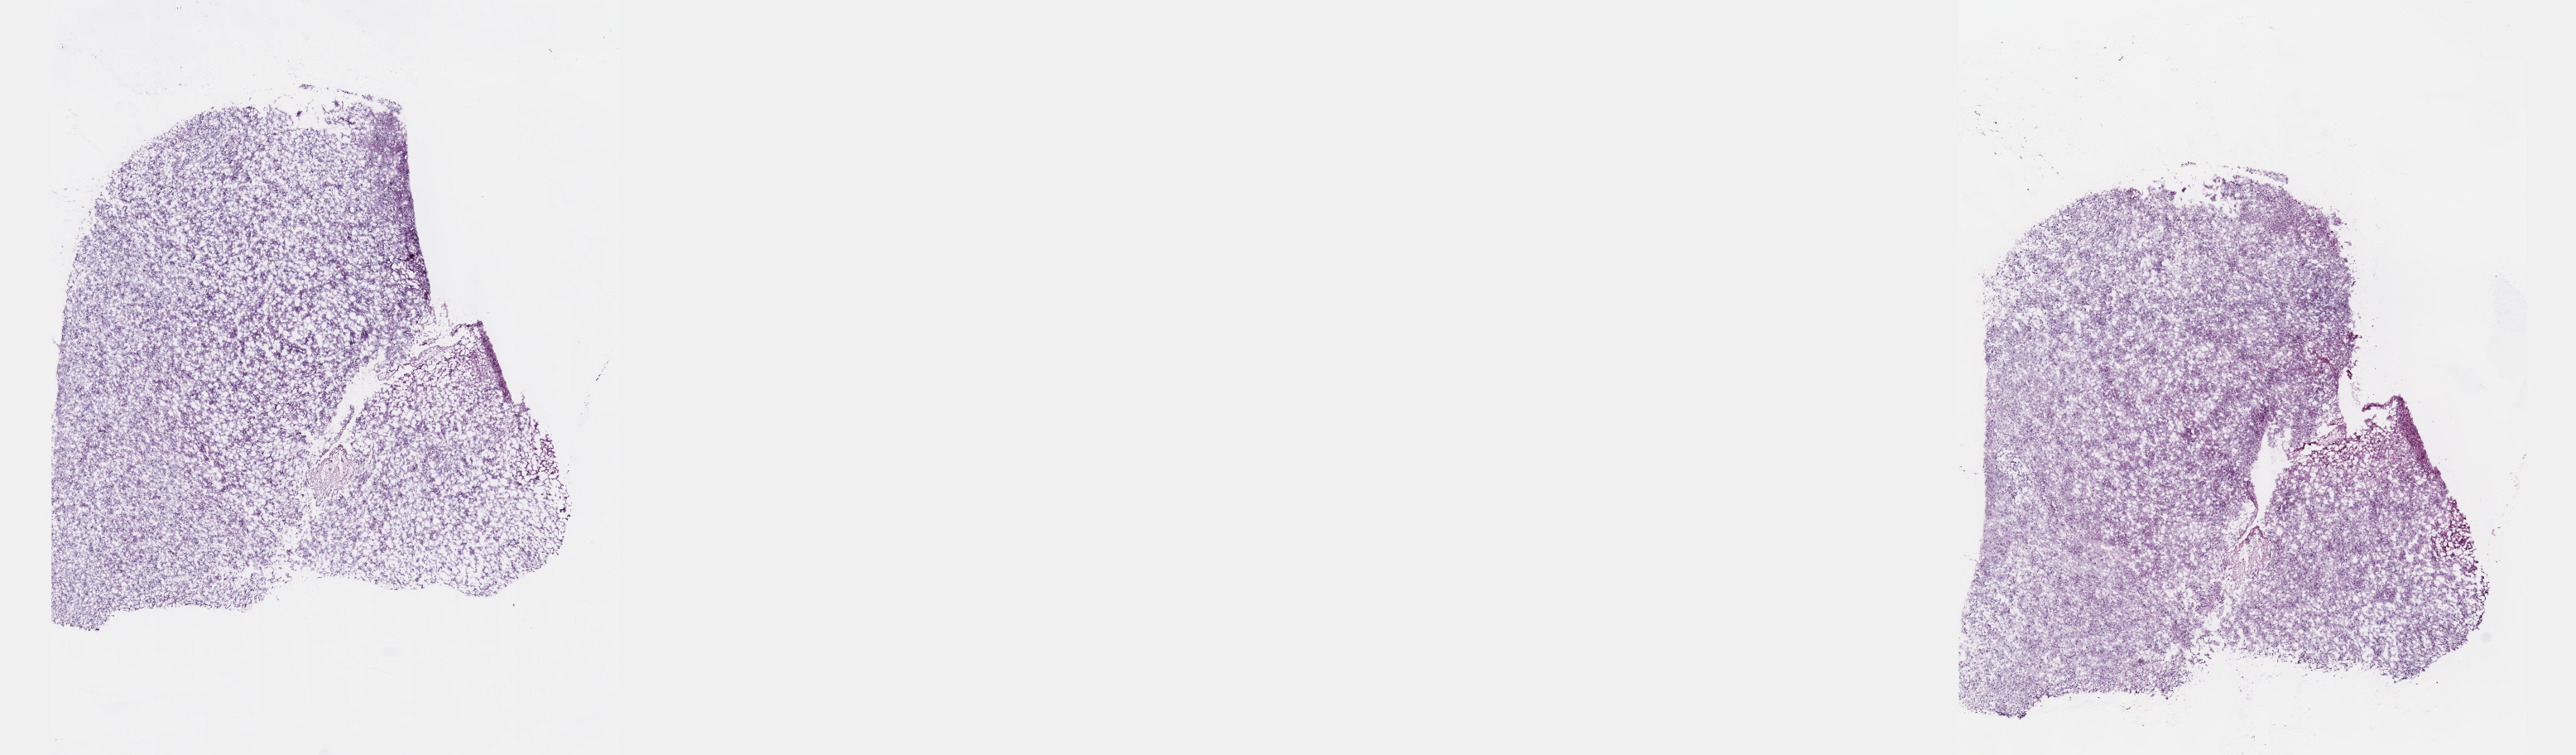
H&E-stained whole-slide image — a low-resolution overview of the entire scanned area, about 25.1 x 7.4 mm (slide scanned at 40x); frozen section from the top of the tissue portion; sample: primary tumour, brain. Female, age 40 years at initial diagnosis. Histologic grade: G2 (moderately differentiated). Slide review estimates, as recorded: tumour cells 50%, tumour nuclei 85%, normal cells 10%, stromal cells 40%, necrosis 0%. Infiltration values recorded for this section: lymphocyte infiltration 0%, monocyte infiltration 0%, neutrophil infiltration 0%.
Diagnosis: Mixed glioma (cerebrum).